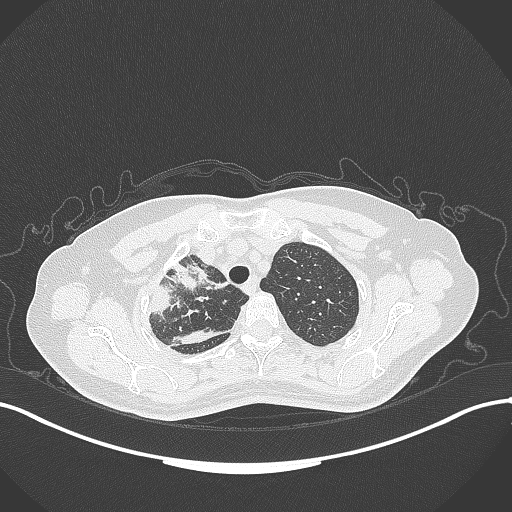
Chest CT, one axial slice; position 265 of 309 along the scan axis; lung window (W 1500 / L -600 HU); 1 mm slice thickness; 512 × 512 image matrix. Patient: female, 60 years. Case-level facts recorded for this patient, not image findings: clinical TNM (as recorded): T3 N1 M1.
Outlined on this slice (bounding box drawn by a radiologist):
- lung tumour (recorded histology: adenocarcinoma): bounding box (x1, y1, x2, y2) in pixels: (161, 253, 224, 292)